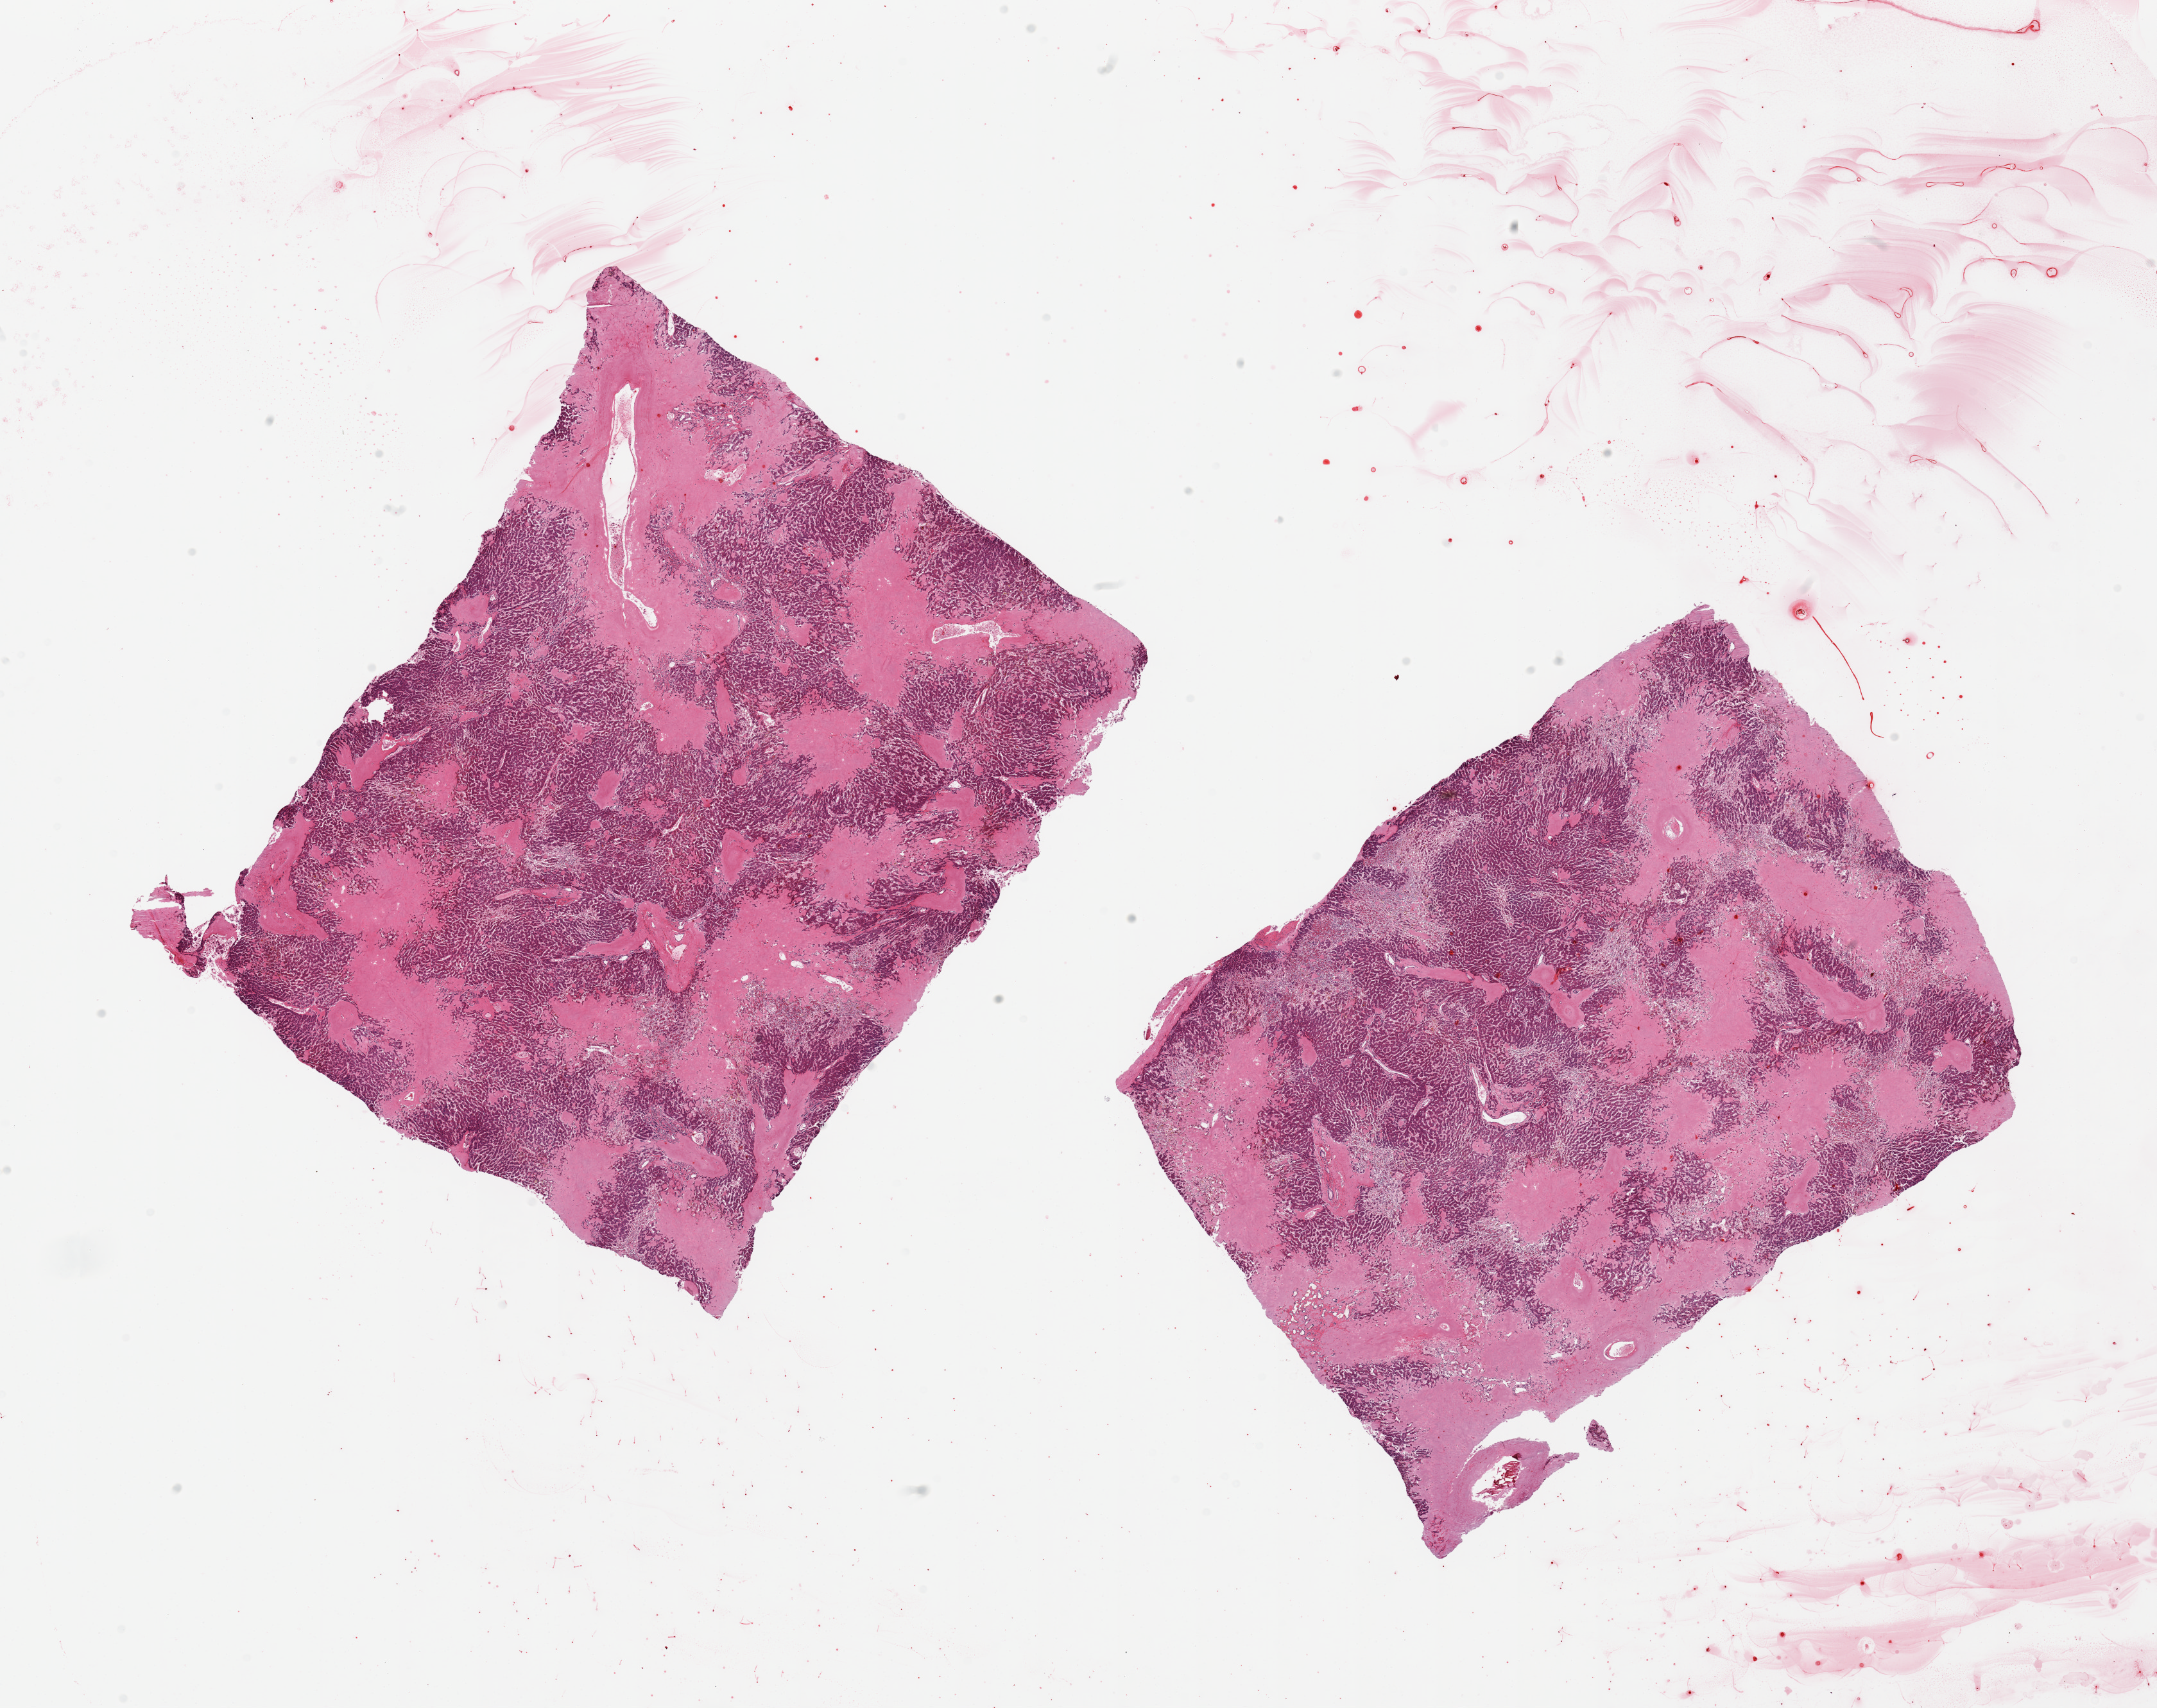
Haematoxylin and eosin whole-slide image — a low-resolution overview of the entire scanned area, about 26.6 x 21.0 mm (acquisition: 20x scan). PAXgene-fixed, paraffin-embedded tissue. Sampled site (target tissue): liver. Donor tissue sample. Donor sex: male.
Pathologist's review note for this sample: 2 pieces, diffuse infiltrative process suggestive of amyloid.